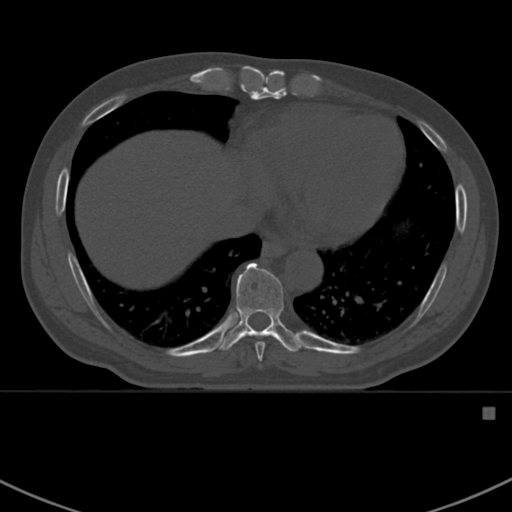
CT including the spine, one axial slice. Position 388 of 412 along the scan axis. Reconstruction kernel Br40s. 120 kVp. Bone window (W 1800 / L 400 HU). 1.5 mm slice thickness. 512 × 512 image matrix, field of view 358 × 358 mm. Male patient, age 59 years. From the clinical record (not read from this slice): primary cancer: prostate.
Structures marked on this image (semi-automatic segmentation, software-assisted and operator-edited):
- T8 vertebra: bounding box [x1, y1, x2, y2] px = [255, 342, 265, 362]
- T9 vertebra: [216, 262, 305, 353]